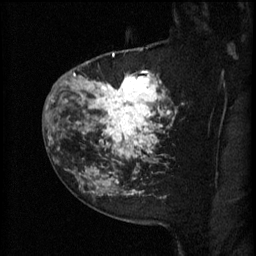
Breast MRI (dynamic contrast-enhanced), one sagittal slice; position 44 of 60 along the scan axis; 3 images stored at this slice position (order not interpretable as contrast timing); 1.5 T; TE 4.2 ms, TR 11 ms; 2 mm slice thickness; 256 × 256 image matrix, field of view 180 × 180 mm. Female patient, age 52 years.
Structures marked on this image (semi-automatic segmentation, software-assisted and operator-edited):
- analysis volume of interest (the breast-tissue region the enhancement analysis was run in; not a lesion): box from (x=81, y=52) to (x=174, y=157) px
- tumour enhancement mask (voxels above the 70 % enhancement threshold inside the analysis volume of interest): (x=81, y=54)–(x=174, y=157)